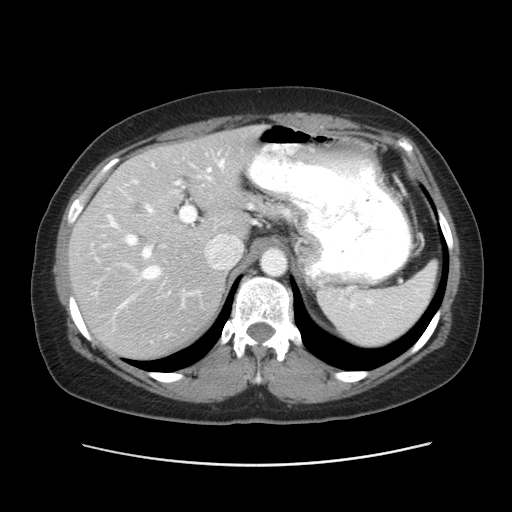
Contrast-enhanced abdominal CT, one axial slice; slice 36 of 52 in the series (ordered by position); reconstruction kernel STANDARD; intravenous contrast given; soft-tissue window (W 400 / L 40 HU); 5 mm slice thickness; 512 × 512 image matrix. Female patient, age 48 years. Case-level facts recorded for this patient, not image findings: diagnosis: colorectal cancer liver metastases, imaged before liver resection; multiple liver metastases: yes; largest metastasis: 4.5 cm; chemotherapy before resection: yes.
Annotated regions visible in this slice (outlined manually by an expert reader):
- hepatic veins: bounding box [x1, y1, x2, y2] px = [119, 160, 224, 308]
- liver: [70, 128, 256, 359]
- planned liver remnant (the part of the liver to remain after resection): [143, 128, 257, 234]
- portal vein (with intrahepatic branches): [98, 168, 211, 295]
- liver metastasis: [135, 202, 145, 214]